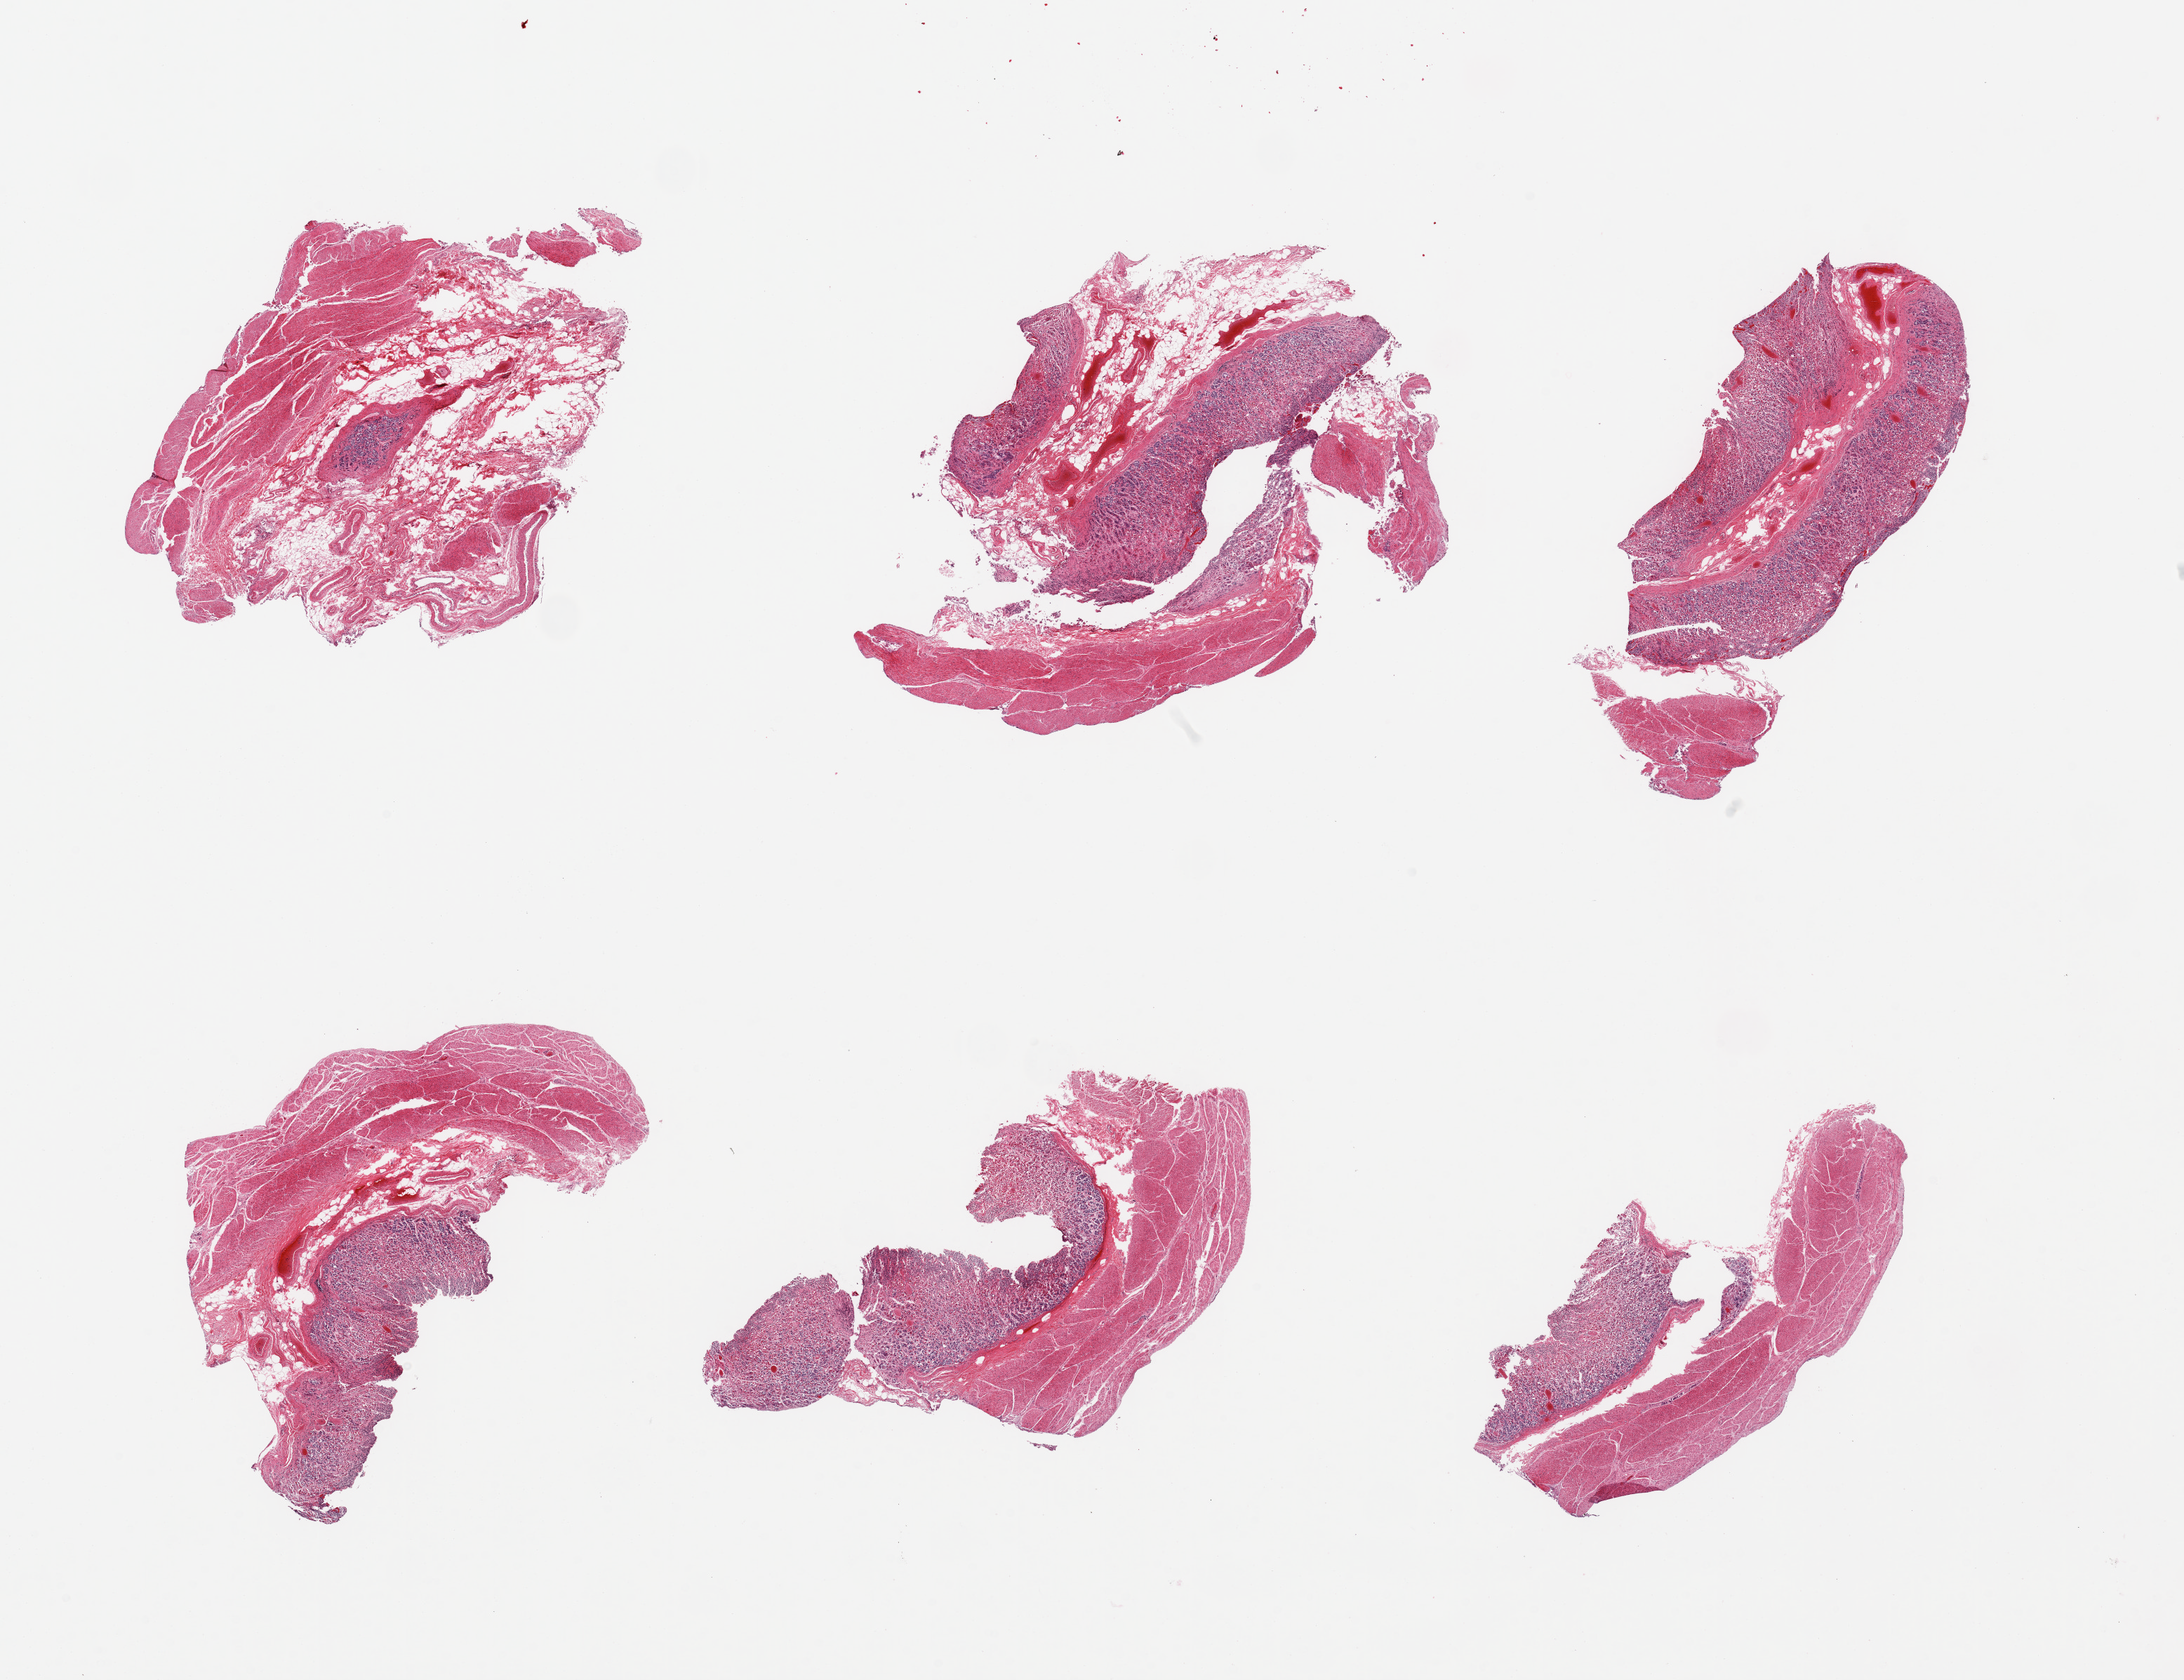
Whole-slide image, H&E stain, whole scanned area (about 24.6 x 18.9 mm, from a 20x scan) shown as a low-resolution overview, PAXgene-fixed, paraffin-embedded tissue, sampled site (target tissue): stomach, donor tissue sample. Donor: male.
Reviewer comment on this tissue sample: 6 pieces, mucosa up to ~1mm, ~50% thickness, moderate-advanced autolysis.